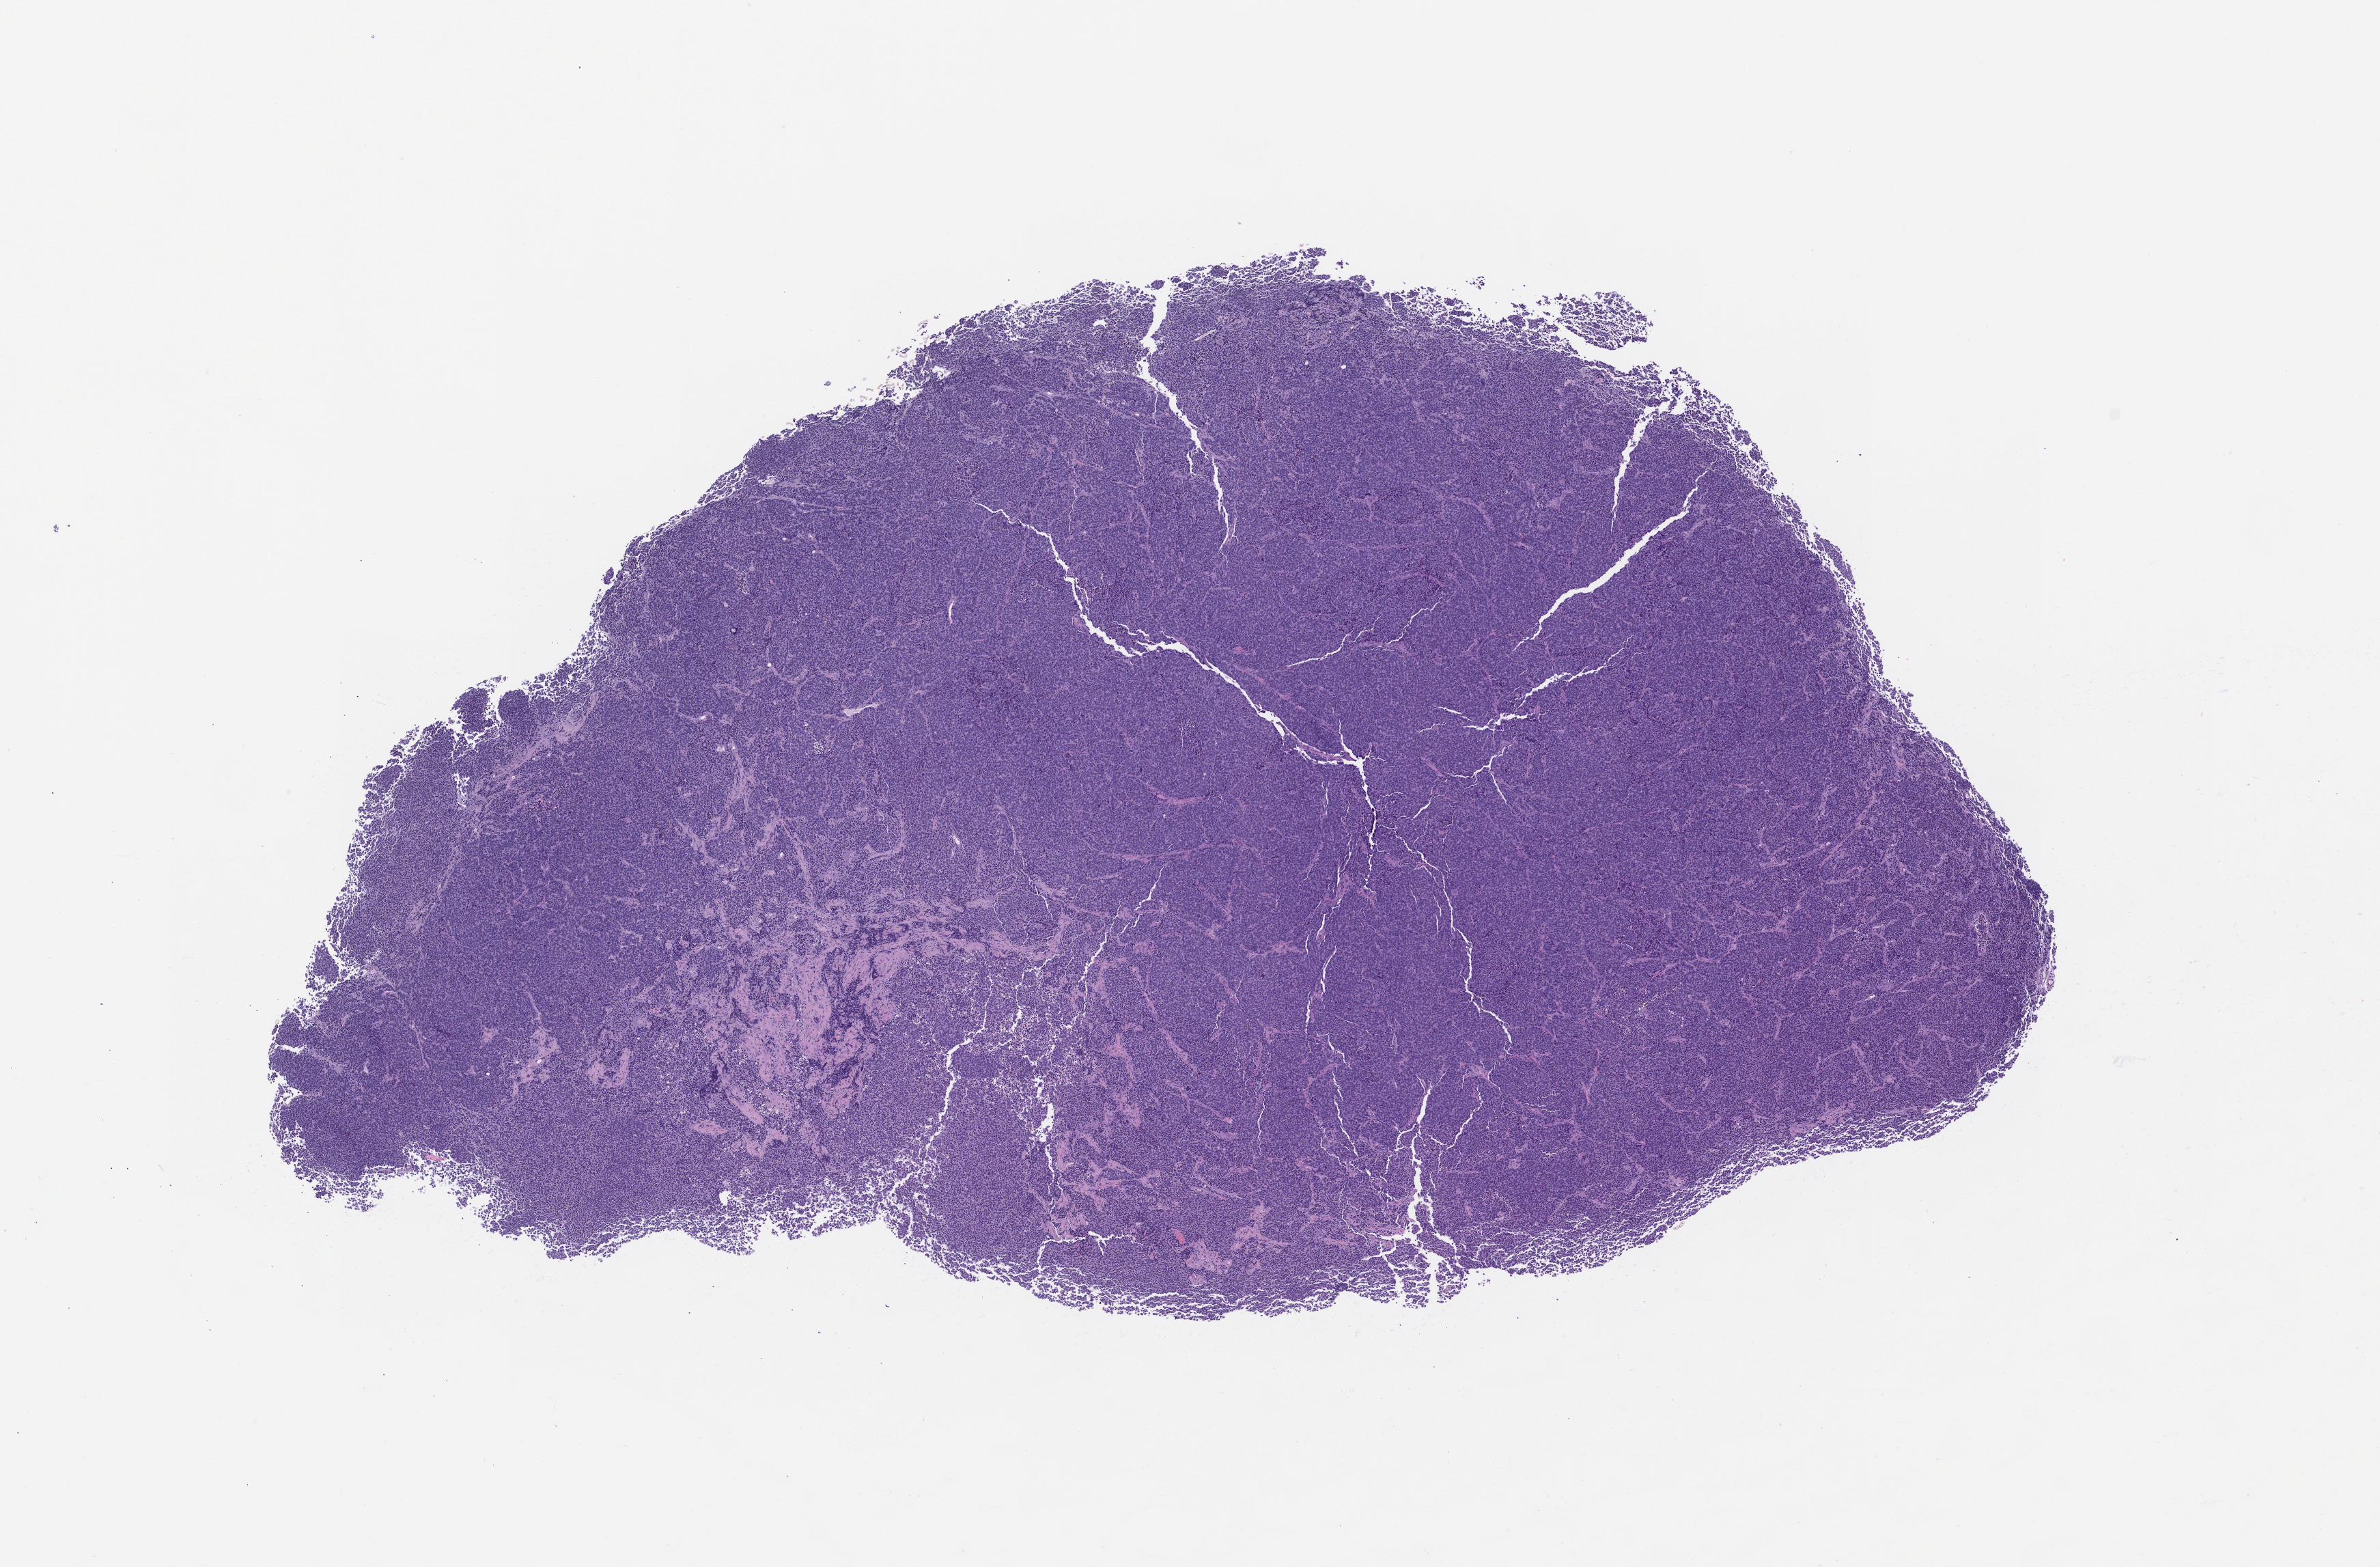
Whole-slide image, H&E: patient-derived xenograft (human tumor grown in a mouse), passage 2, whole scanned area (about 14.0 x 9.2 mm) shown as a low-resolution overview, FFPE section, originating tumor site category: bladder.
• originating patient diagnosis: Bladder Small Cell Neuroendocrine Carcinoma